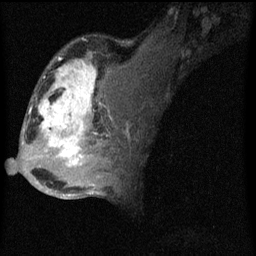
Breast MRI (dynamic contrast-enhanced), one sagittal slice. Position 33 of 60 along the scan axis. Dynamic contrast-enhanced series, image 2 of 4 at this slice position (ordered by acquisition). 1.5 T. TE 4.2 ms, TR 8 ms. 2 mm slice thickness. 256 × 256 image matrix, field of view 180 × 180 mm. Female patient, age 50 years.
Annotated regions visible in this slice (semi-automatic segmentation, software-assisted and operator-edited):
- analysis volume of interest (the breast-tissue region the enhancement analysis was run in; not a lesion): bounding box <26,44,124,177> (left, top, right, bottom; pixels)
- tumour enhancement mask (voxels above the 70 % enhancement threshold inside the analysis volume of interest): <30,60,113,167>